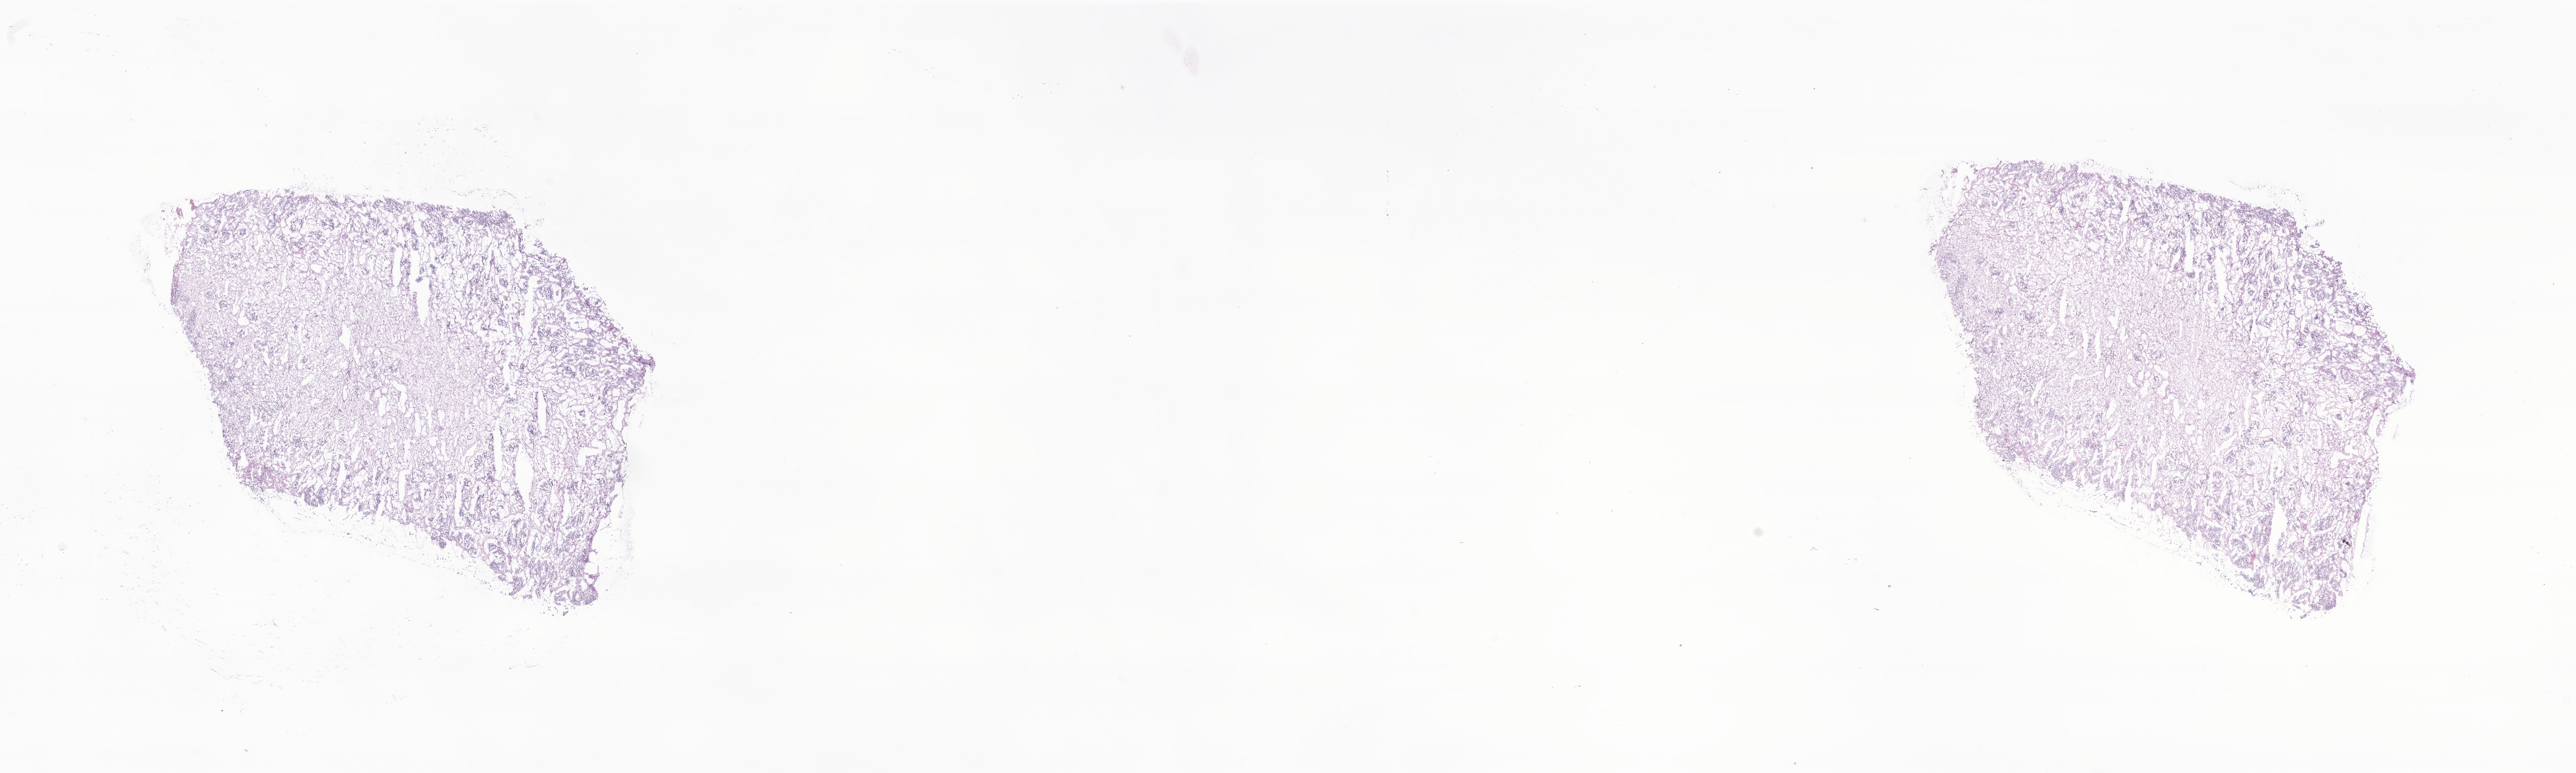
Whole-slide image, haematoxylin and eosin stain of tumor tissue from the adrenal gland — whole scanned area (about 30.2 x 9.1 mm) shown as a low-resolution overview; frozen section (OCT-embedded). Patient: female, age 120 days.
* diagnosis: Neuroblastoma, NOS